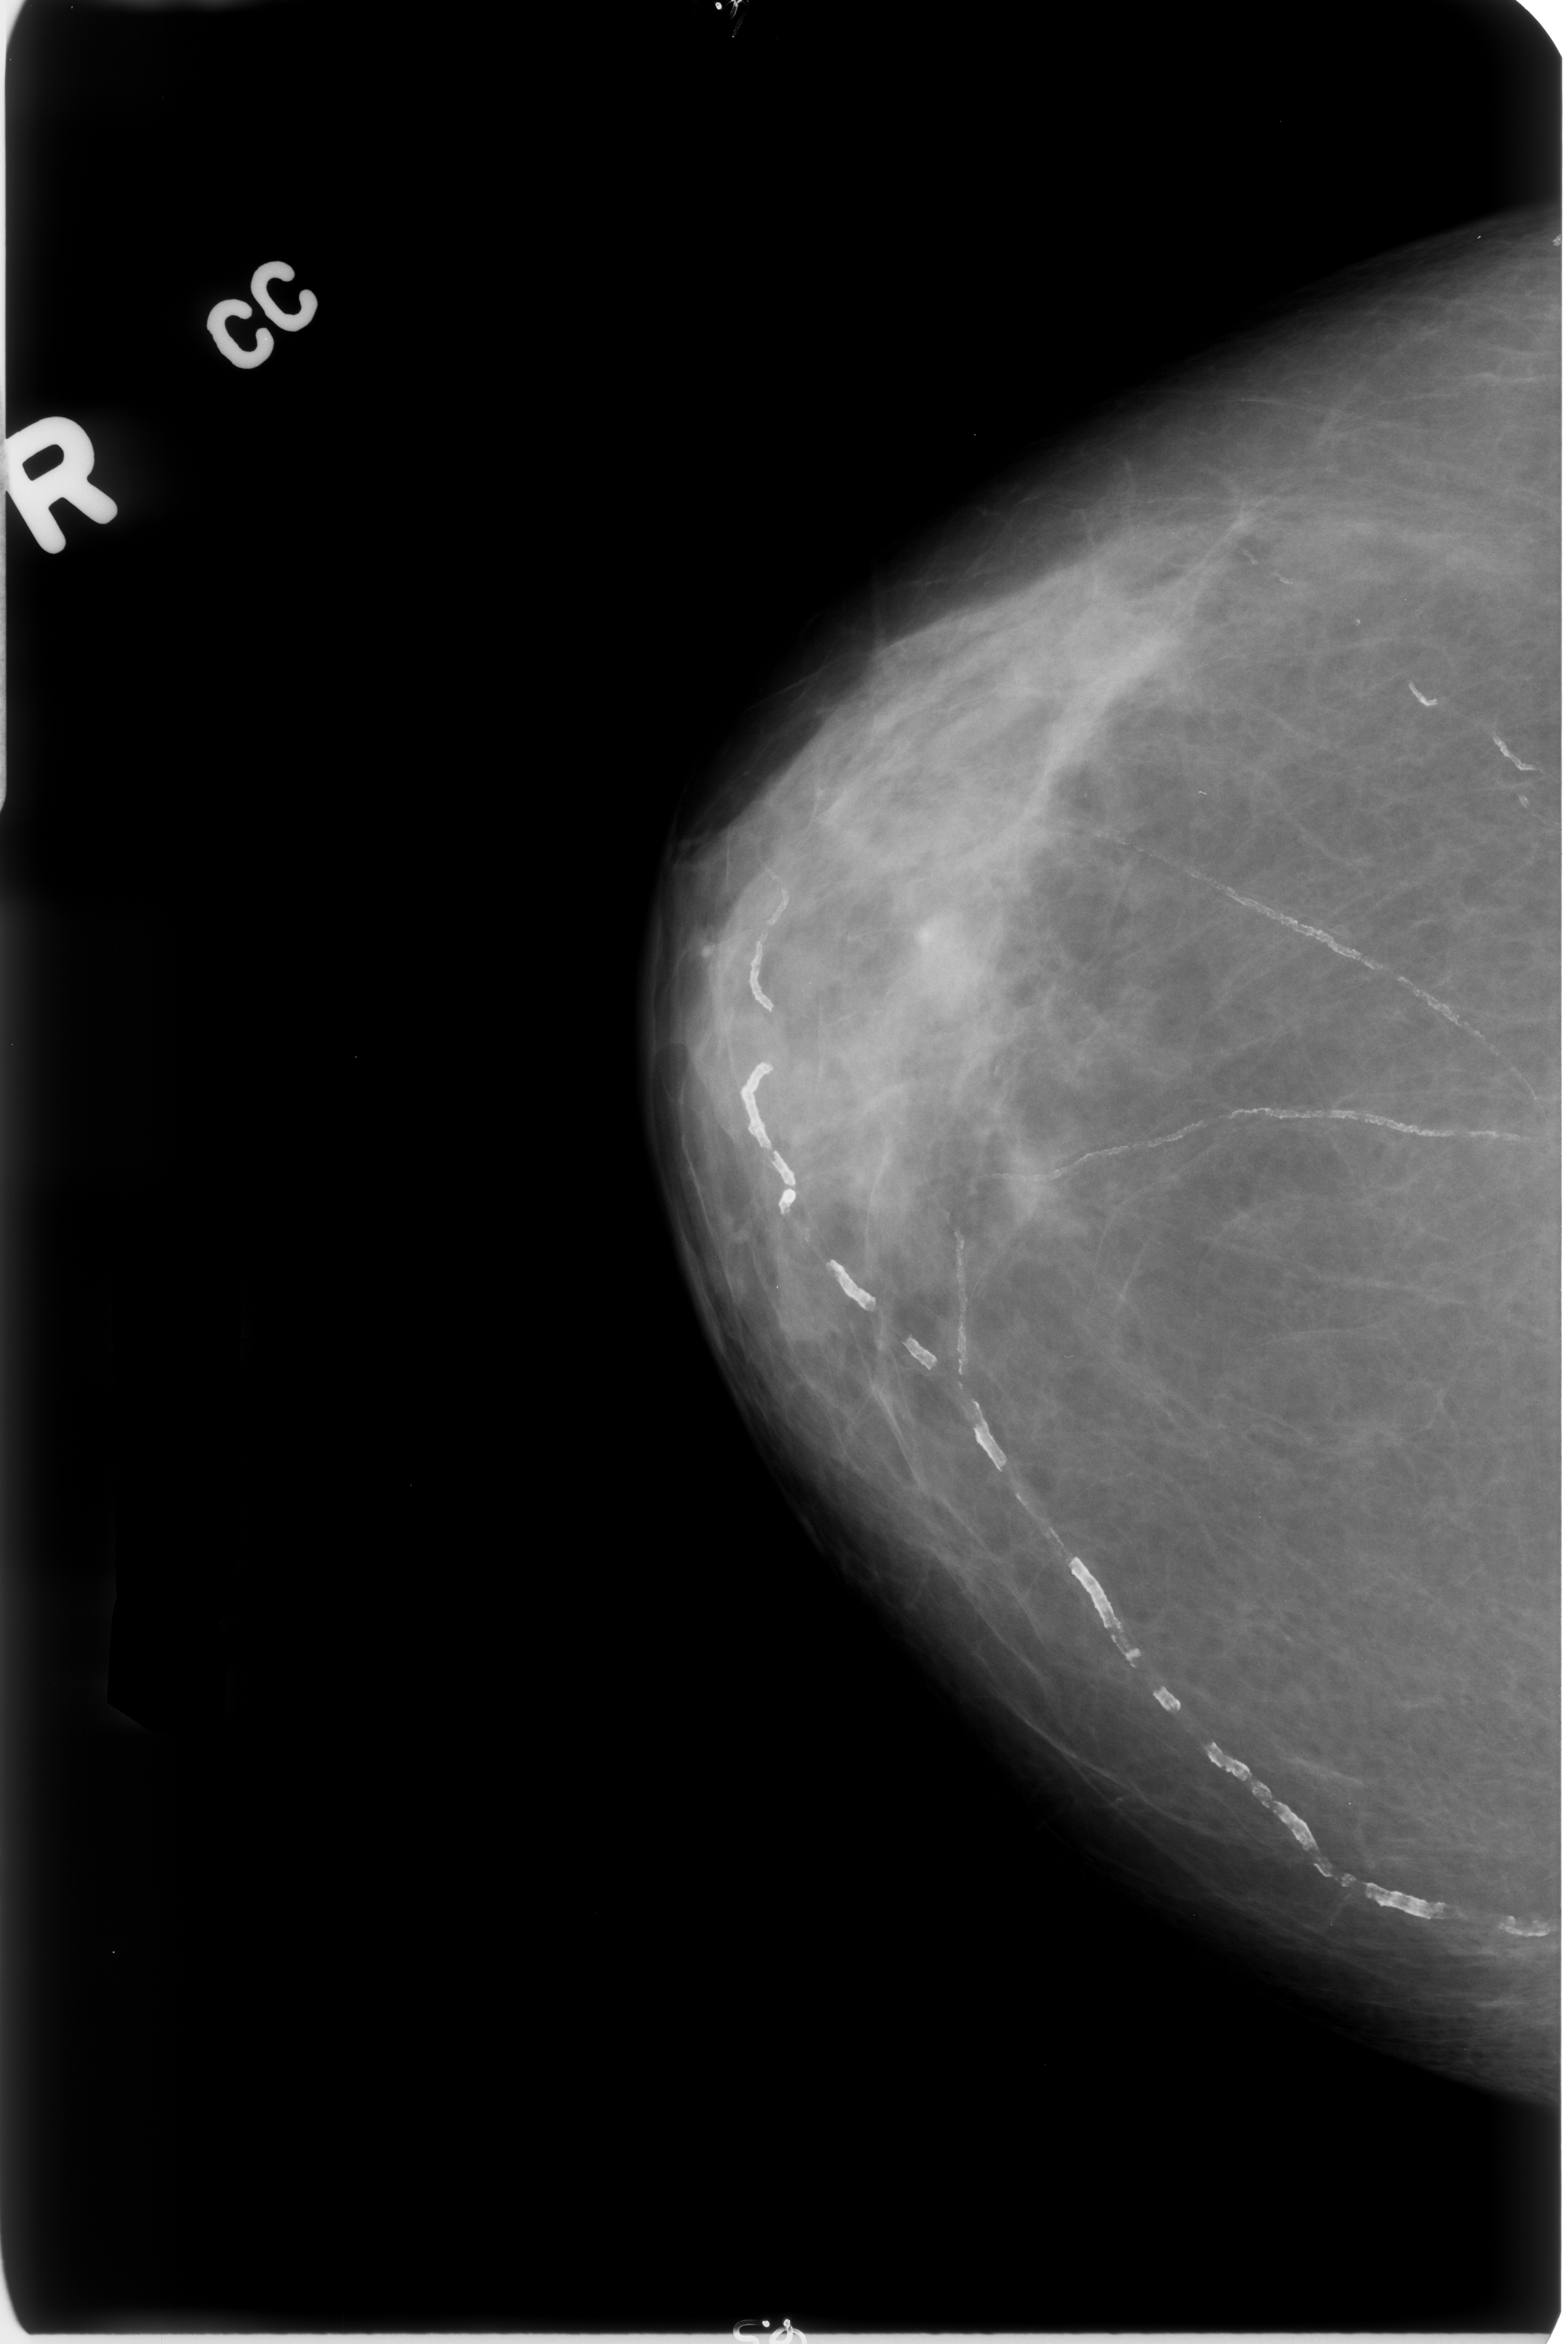
Scanned film-screen mammogram, right breast, CC view.
Marked findings (only marked abnormalities are described; nothing is implied about the rest of the image): Finding 1 of 3: calcifications, morphology vascular; BI-RADS assessment category 2; benign; no additional work-up was recommended (benign without callback). Finding 2 of 3: calcifications, morphology vascular; BI-RADS assessment category 2; benign; no additional work-up was recommended (benign without callback). Finding 3 of 3: calcifications, morphology vascular; BI-RADS assessment category 2; benign without callback (not worked up further).